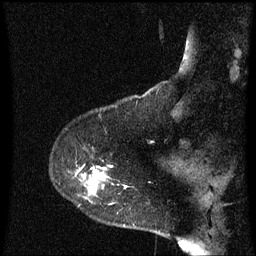
Breast MRI (dynamic contrast-enhanced), one sagittal slice; position 14 of 60 along the scan axis; dynamic contrast-enhanced series, image 2 of 3 at this slice position (ordered by acquisition); 1.5 T; TE 4.2 ms, TR 8.9 ms; 2 mm slice thickness; 256 × 256 image matrix, field of view 200 × 200 mm. Patient: female, 53 years. Case-level facts recorded for this patient, not image findings: setting: breast cancer imaged before/during neoadjuvant chemotherapy; receptor status: HR-positive, HER2-negative.
Structures marked on this image (semi-automatic segmentation, software-assisted and operator-edited):
- analysis volume of interest (the breast-tissue region the enhancement analysis was run in; not a lesion): bounding box [x1, y1, x2, y2] px = [76, 162, 129, 227]
- tumour enhancement mask (voxels above the 70 % enhancement threshold inside the analysis volume of interest): [88, 172, 97, 191]